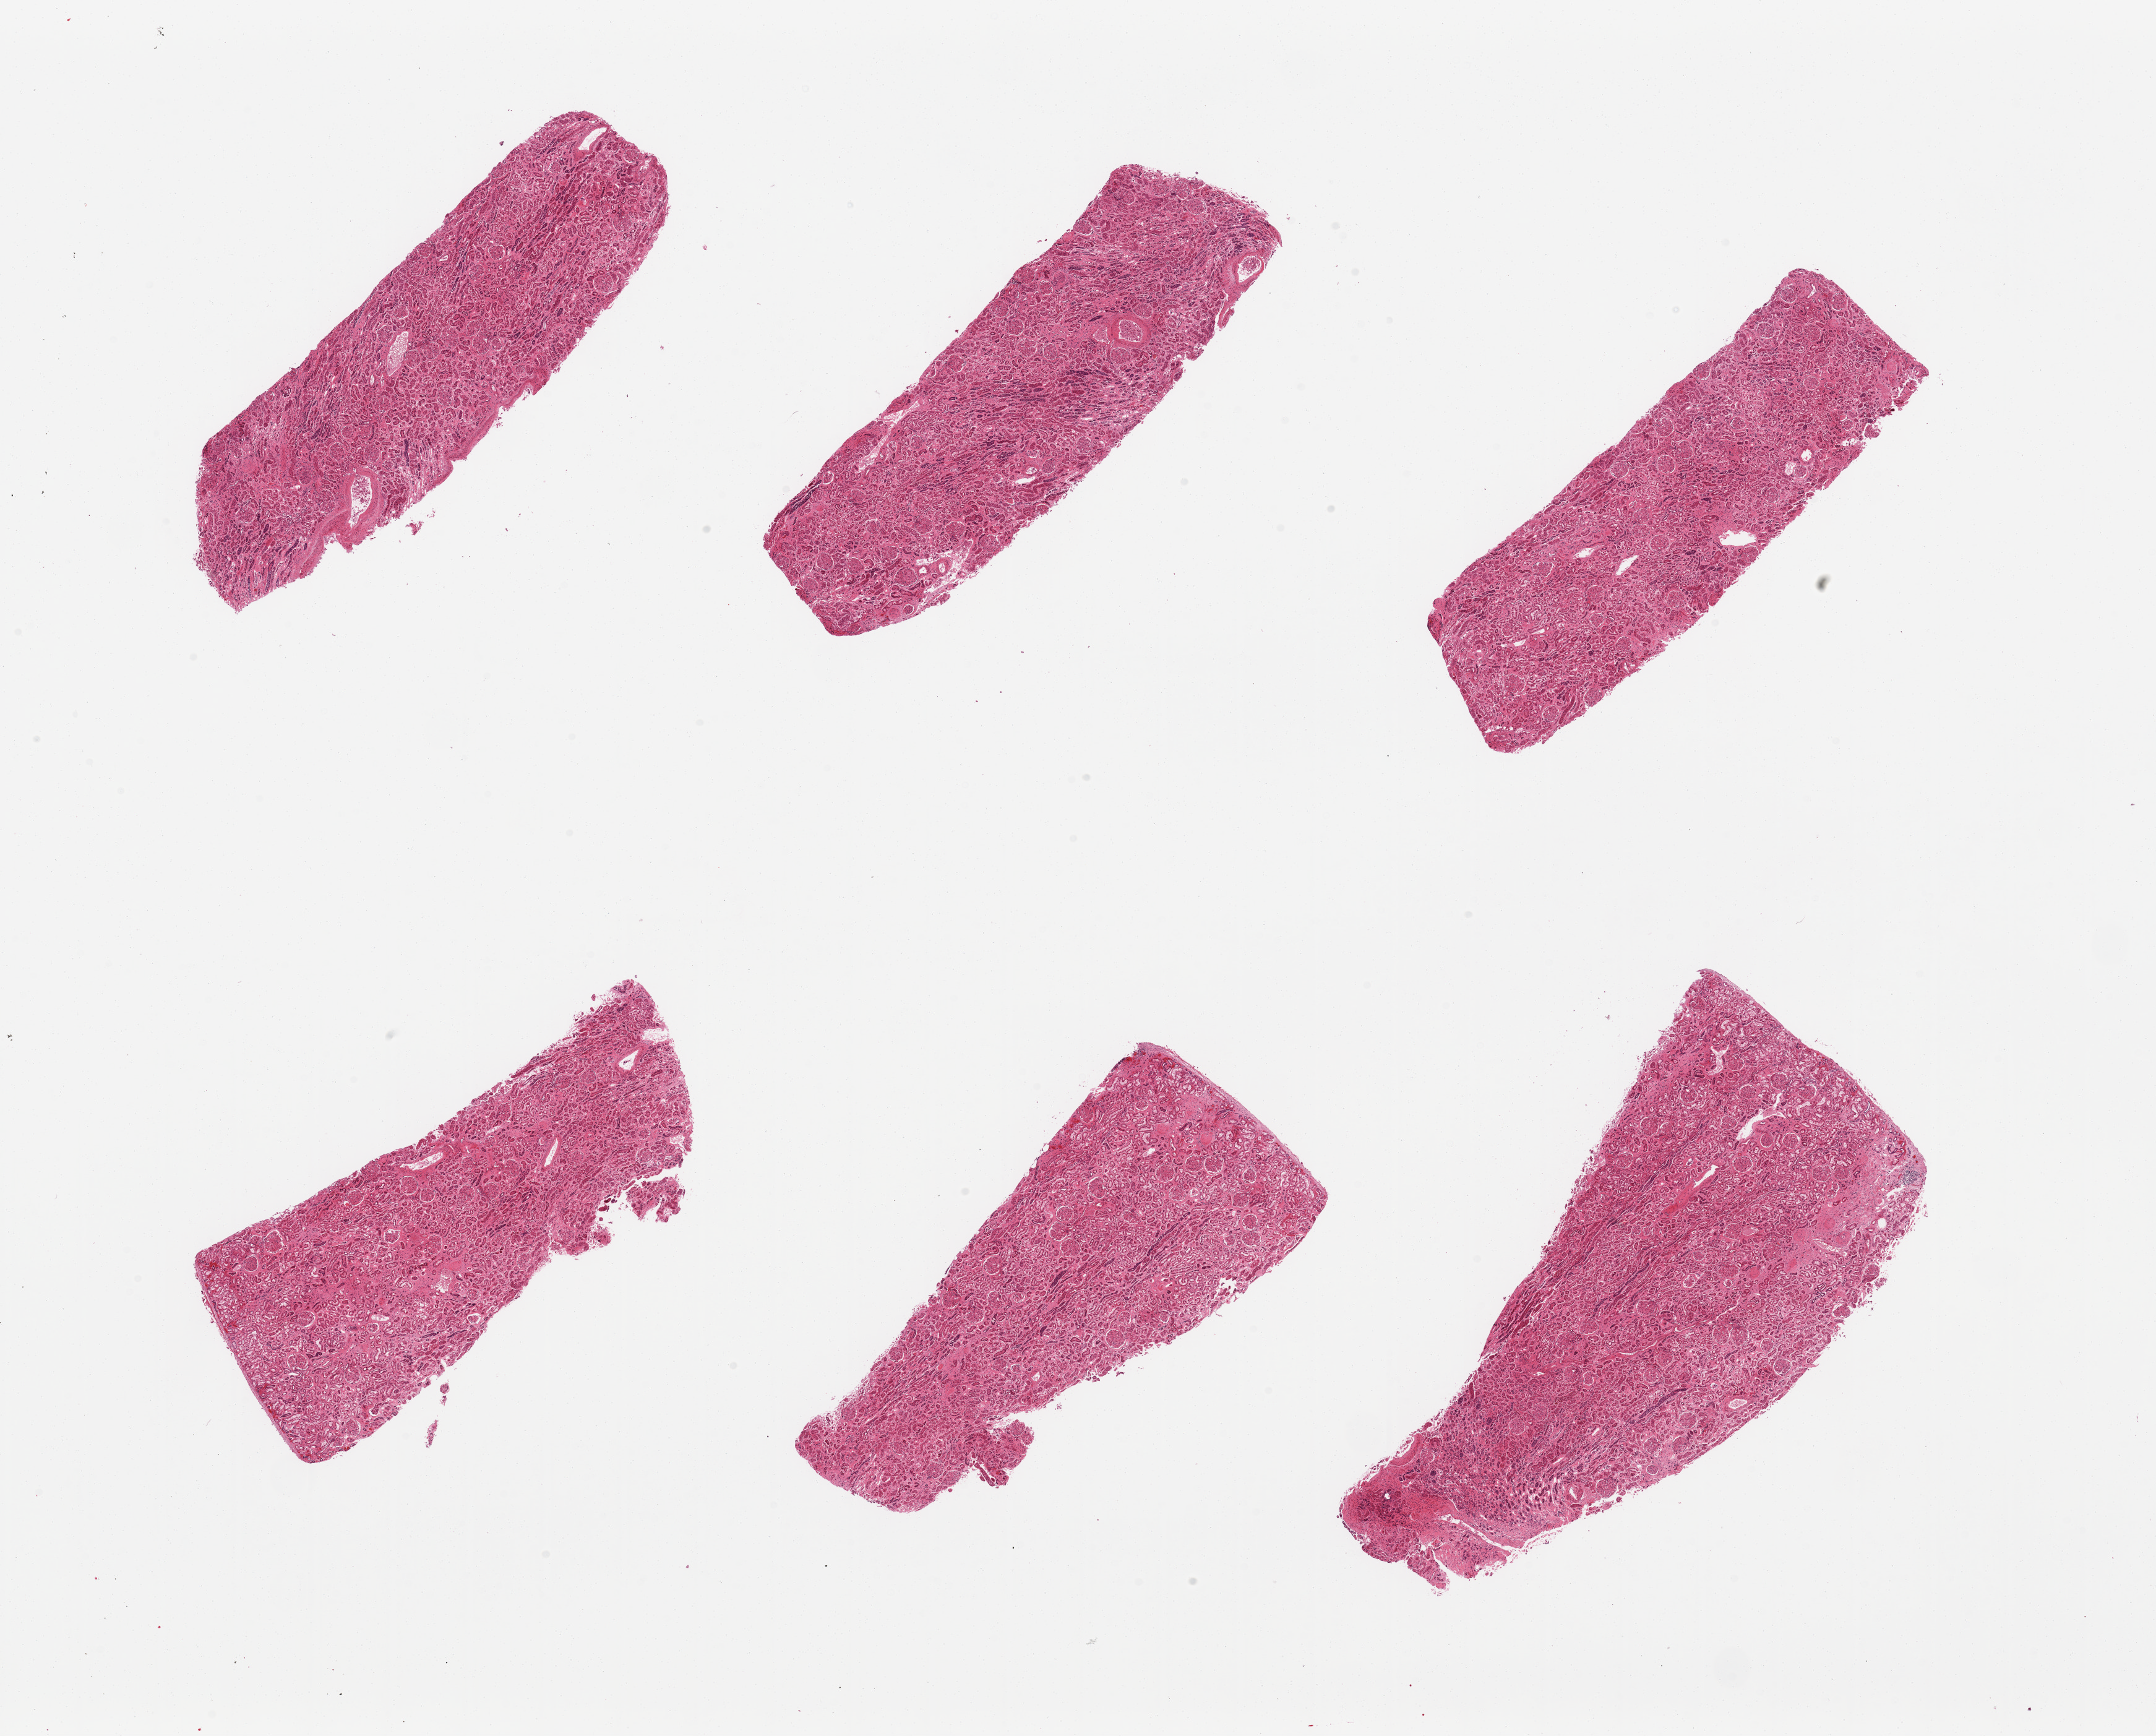
Hematoxylin and eosin (H&E) whole-slide image, brightfield — a low-resolution overview of the entire scanned area, about 27.6 x 22.2 mm (acquisition: 20x scan), PAXgene-fixed paraffin-embedded (PFPE) section, section of renal cortex (target tissue), tissue donor sample. Male donor.
- reviewer comment on this tissue sample: 6 pieces, glomeruli present in all